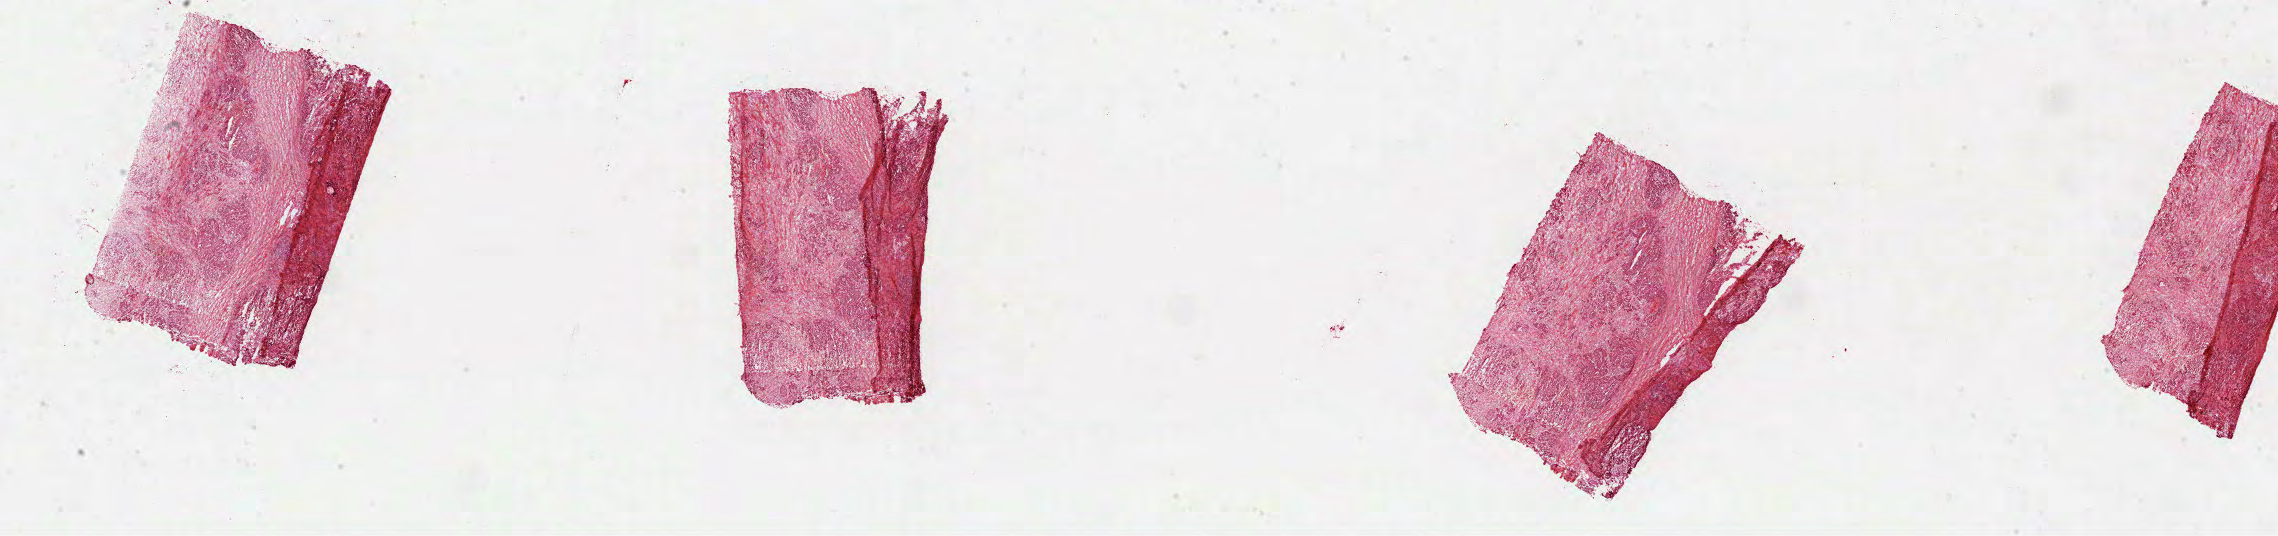
Digitized Hematoxylin and eosin (H&E) stained tissue section (whole slide), a low-resolution overview of the entire scanned area, about 36.7 x 8.6 mm (acquisition: 40x scan). FFPE section. Sample: primary tumour, rectum. Male, age 33 years at initial diagnosis.
TNM: T3 N1 M0. Pathologic diagnosis: Adenocarcinoma with mixed subtypes. AJCC pathologic stage: IIIA (7th edition). Lymph nodes positive (case pathology): 3 of 14 examined.